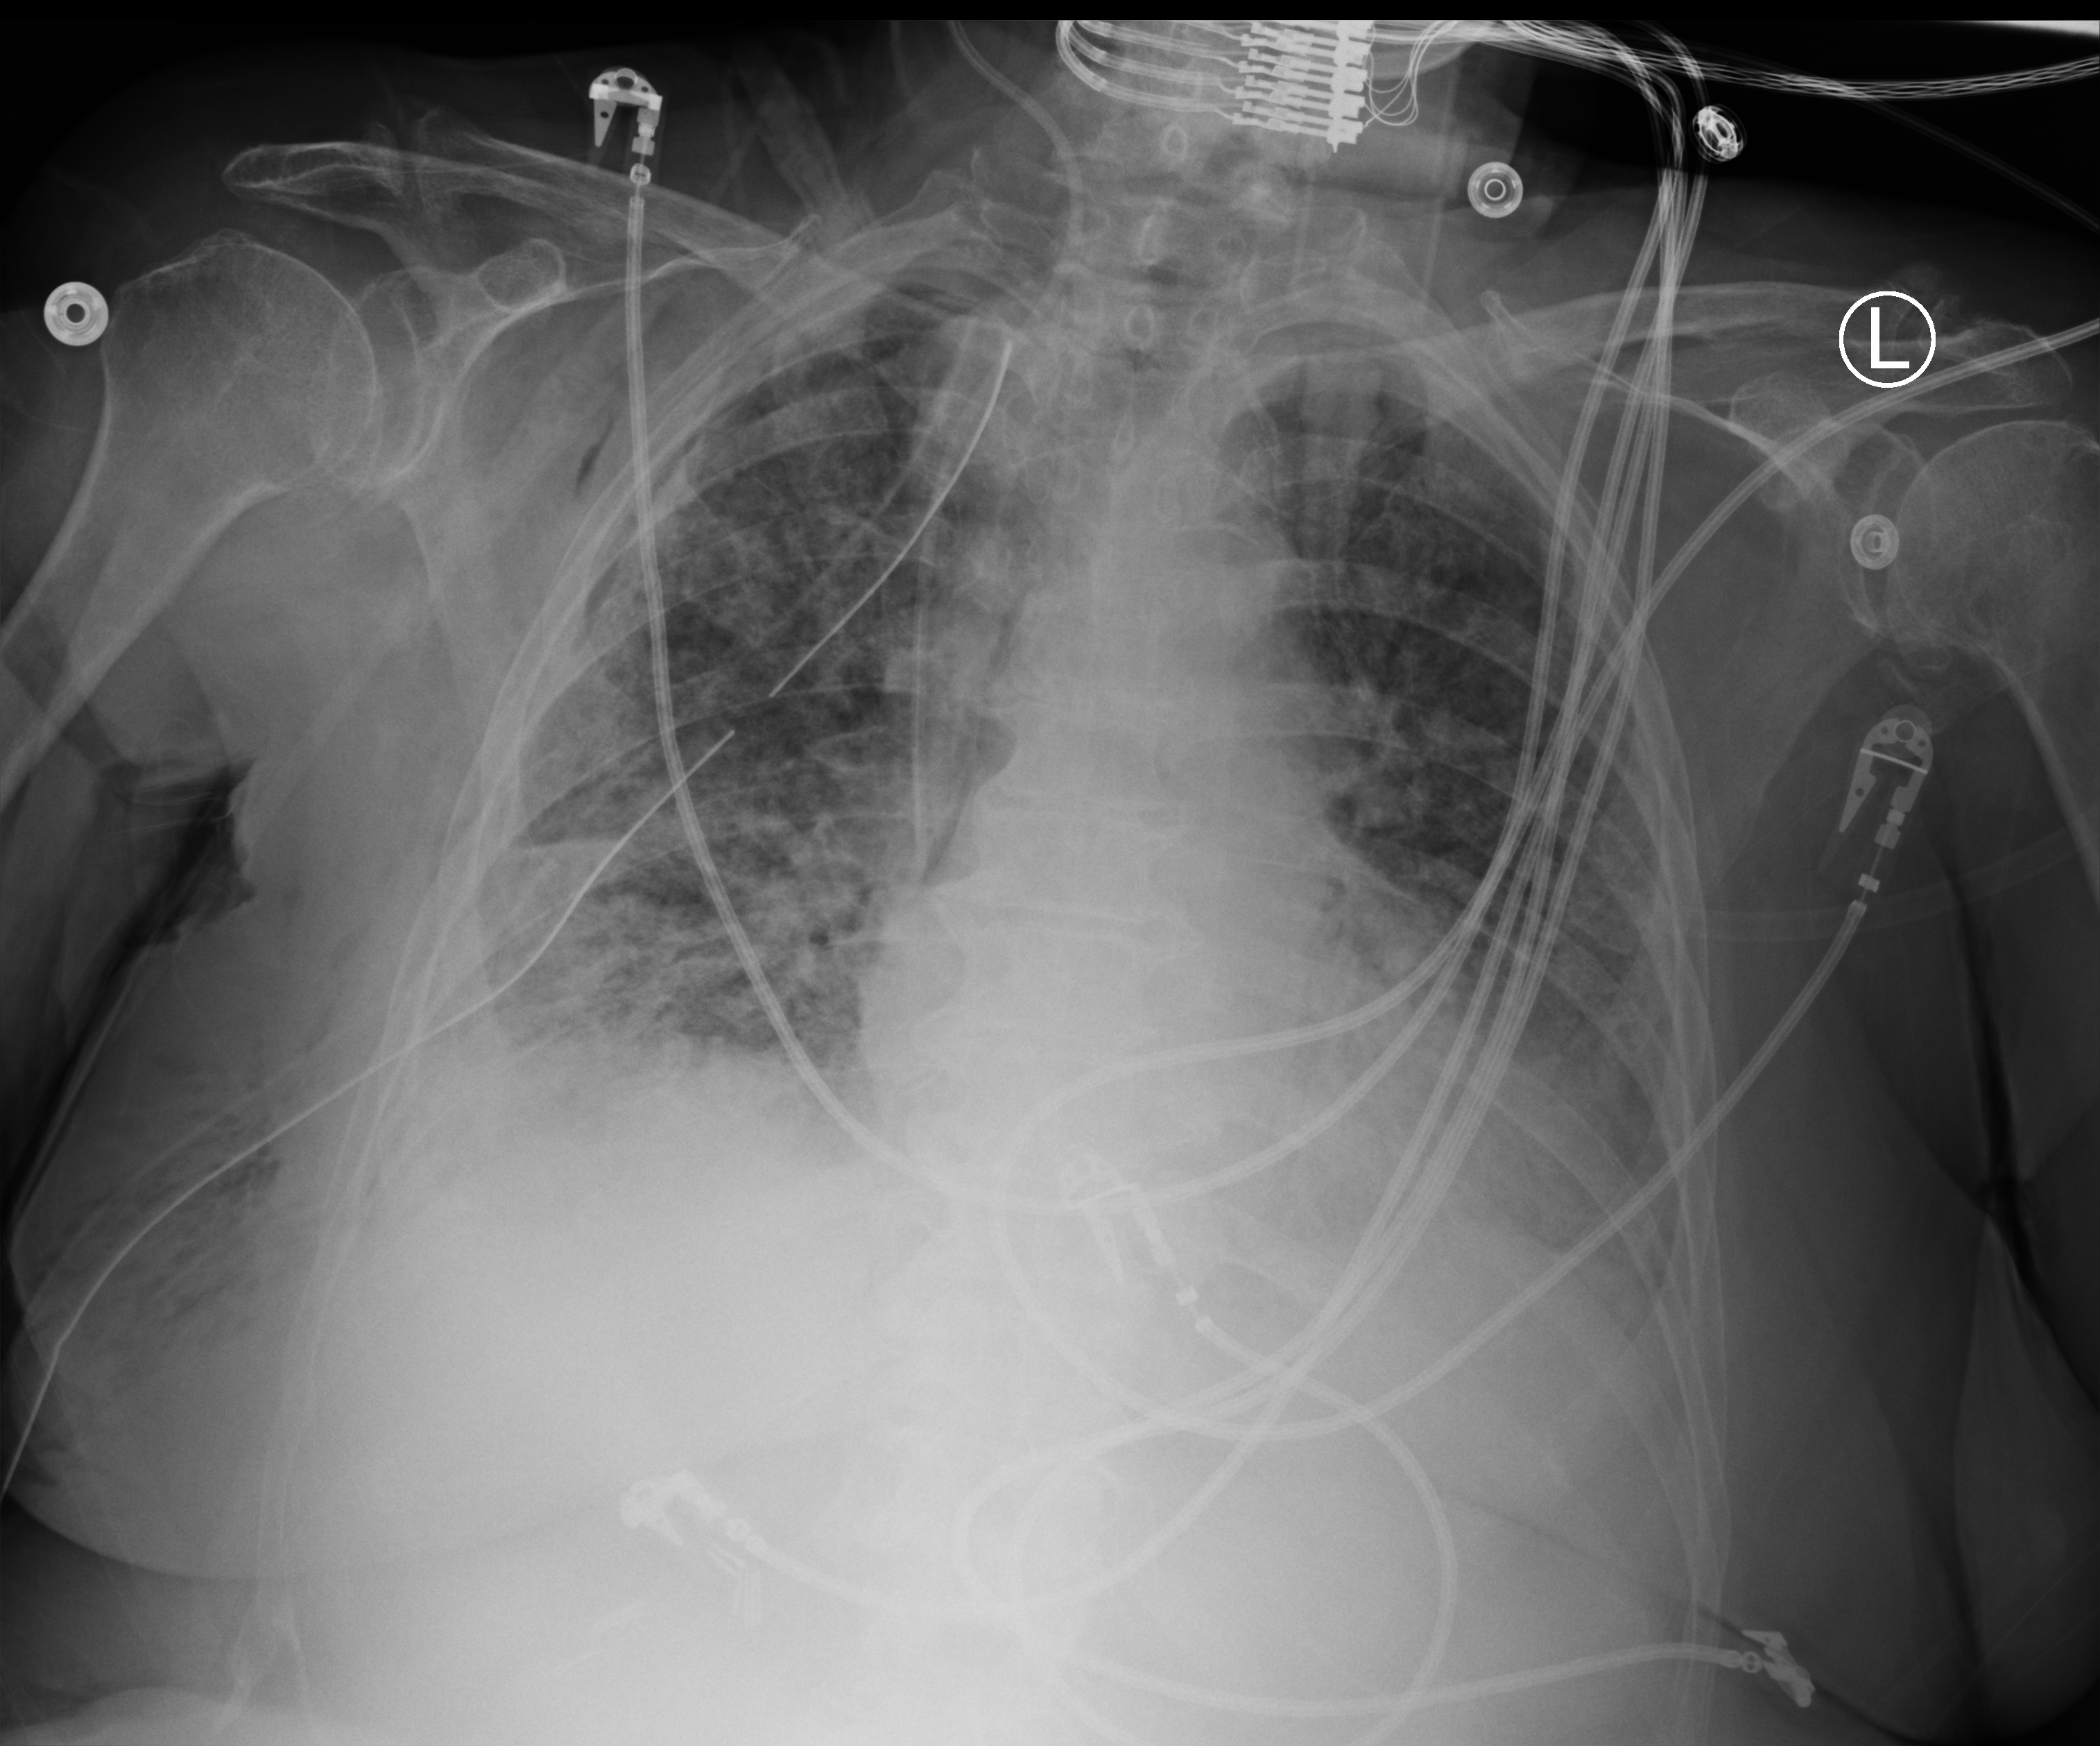
Portable chest radiograph; anteroposterior (AP) projection. Patient hospitalised with COVID-19; female, aged 75–90 years.
Admission-level facts for this patient (not findings on this image; timing relative to this image not recorded): mechanically ventilated during this hospital stay: yes; diabetes (admission record): no.